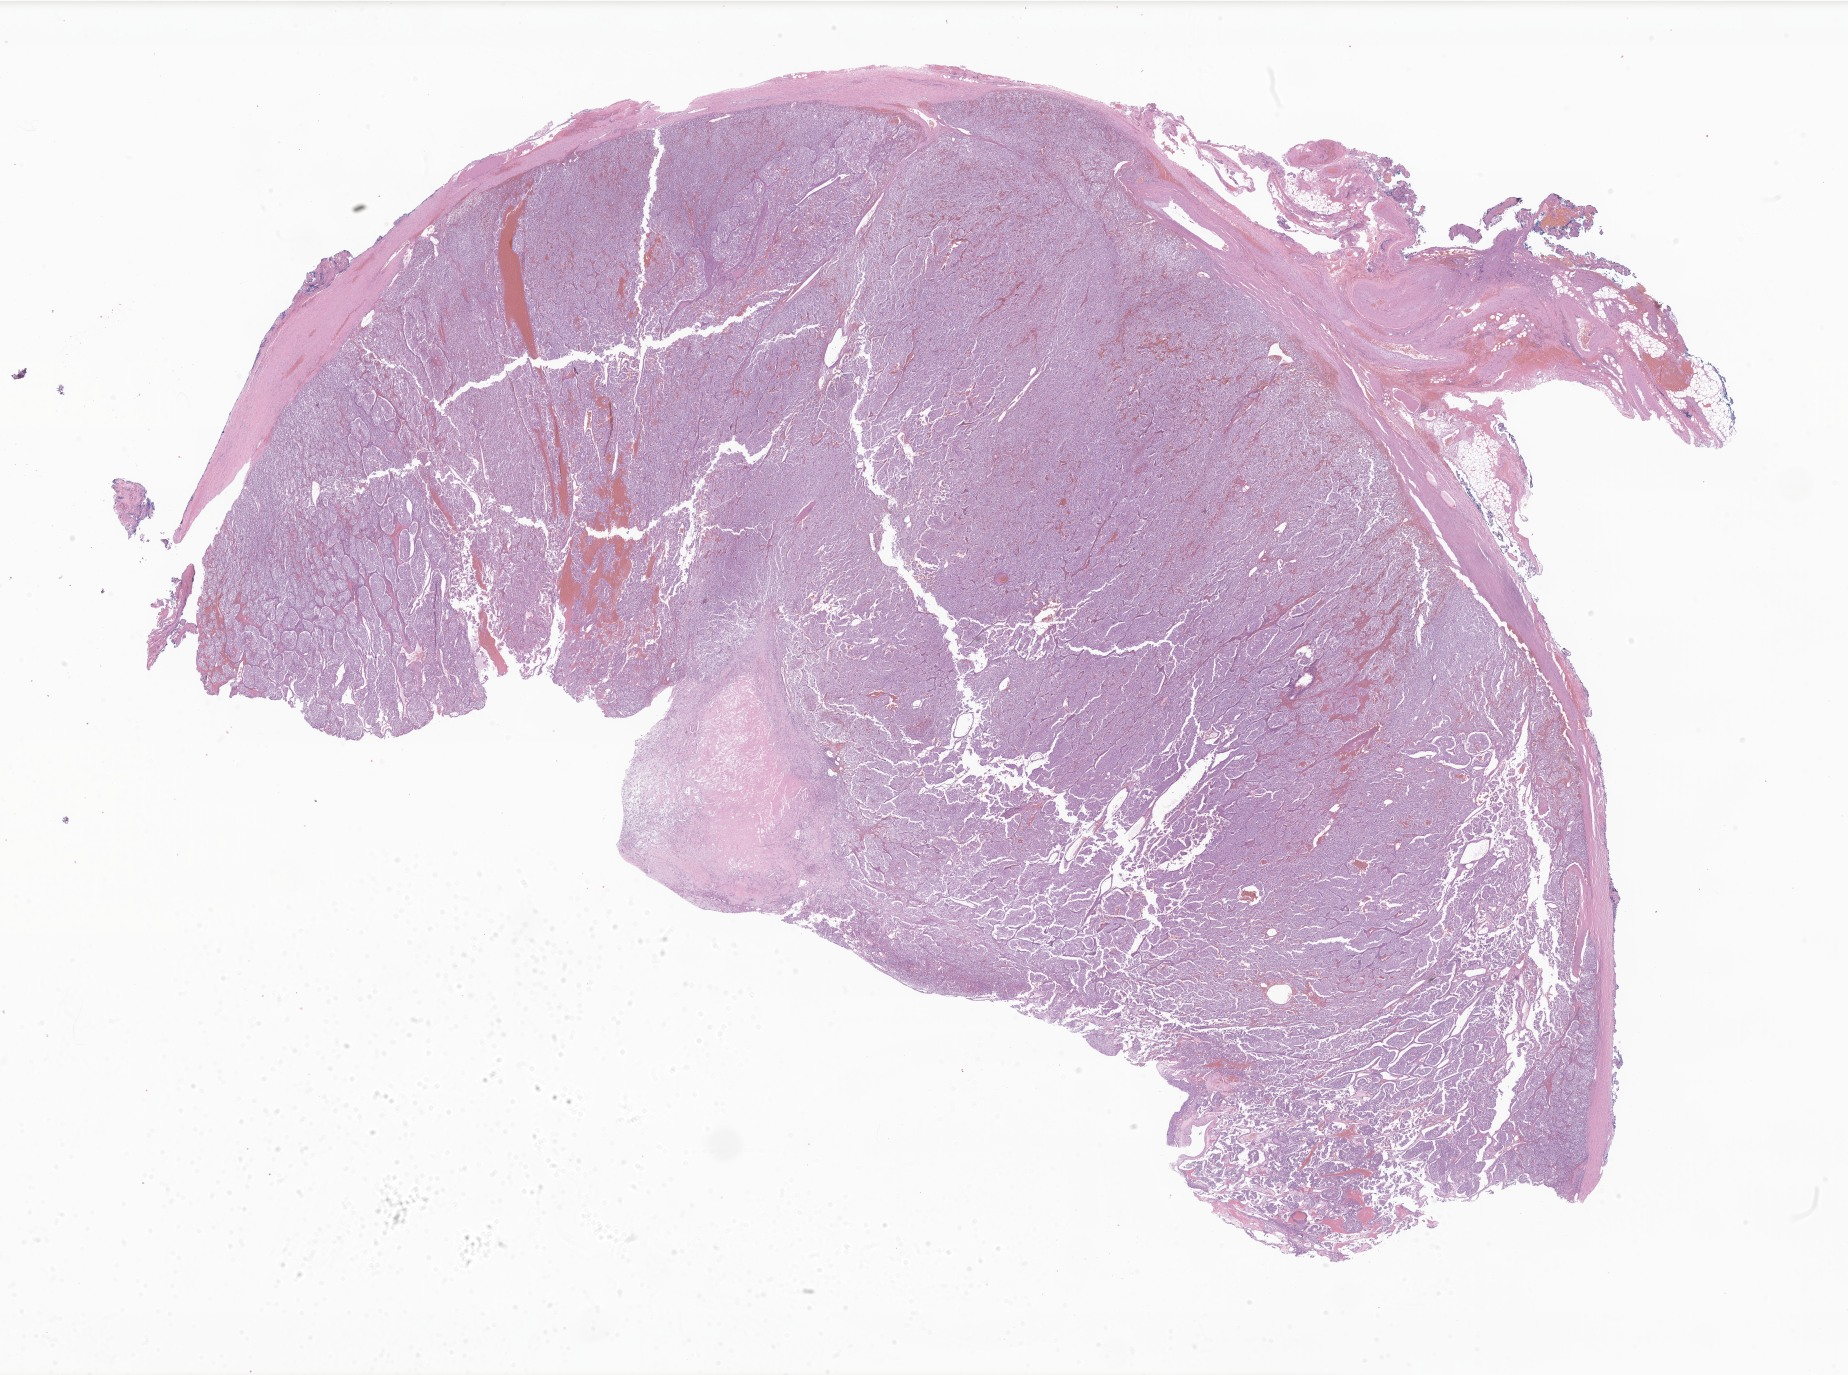
Haematoxylin and eosin whole-slide image of tumor tissue from the retroperitoneum, a low-resolution overview of the entire scanned area, about 31.2 x 23.2 mm. Formalin-fixed paraffin-embedded section. Patient: female, age 164 months (13 years 8 months).
Diagnosis (ICD-O-3 morphology term): Paraganglioma, NOS.